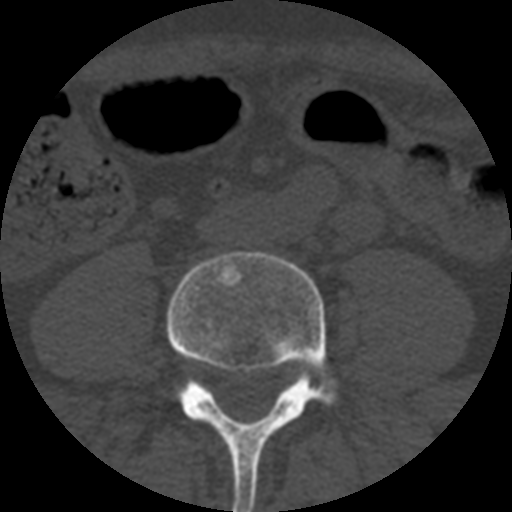
CT including the spine, one axial slice. Slice 89 of 508 in the series (ordered by position). Reconstruction kernel STANDARD. 120 kVp. Bone window (W 1800 / L 400 HU). 1.25 mm slice thickness. 512 × 512 image matrix, field of view 160 × 160 mm. Patient age 57 years. Case-level facts recorded for this patient, not image findings: primary cancer: prostate.
Outlined on this slice (semi-automatically segmented with operator editing):
- L4 vertebra: box from (x=168, y=252) to (x=336, y=512) px